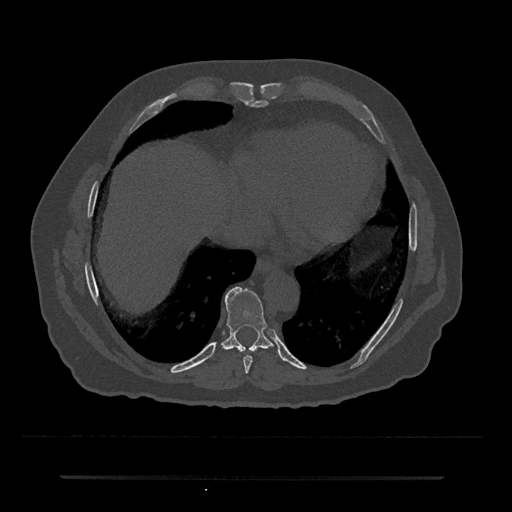
CT including the spine, one axial slice; position 292 of 797 along the scan axis; reconstruction kernel Br40s/3; 120 kVp; bone window (W 1800 / L 400 HU); 0.5 mm slice thickness; 512 × 512 image matrix. Male patient, age 69 years. From the clinical record (not read from this slice): primary cancer: prostate.
Structures marked on this image (semi-automatically segmented with operator editing):
- T8 vertebra: box from (x=243, y=355) to (x=253, y=373) px
- T9 vertebra: (x=222, y=287)–(x=277, y=352)